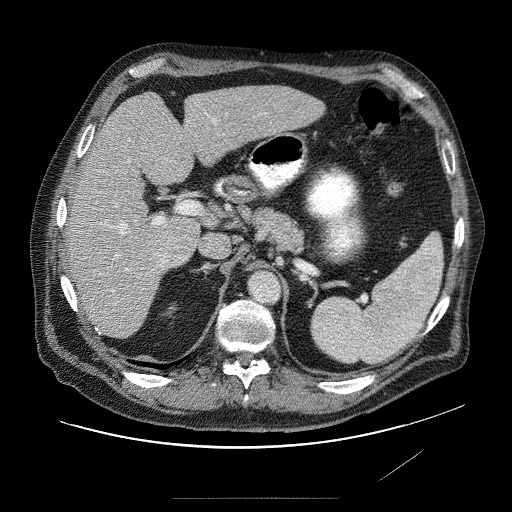
Contrast-enhanced abdominal CT (liver protocol), one axial slice. Slice 45 of 89 in the series (ordered by position). 120 kVp. Soft-tissue window (W 400 / L 40 HU). 2.5 mm slice thickness. 512 × 512 image matrix, field of view 420 × 420 mm. Case-level facts recorded for this patient, not image findings: diagnosis: hepatocellular carcinoma (patient treated with transarterial chemoembolisation; whether this scan precedes or follows treatment is not stated here); TNM stage (as recorded): Stage-IVA; Child-Pugh class: A; tumour differentiation: moderately differentiated.
Annotated regions visible in this slice (semi-automatically segmented with operator editing):
- liver parenchyma outside the tumour (the mass and vessels are separate outlines, so this box may not span the whole liver): bounding box [x1, y1, x2, y2] px = [62, 84, 326, 336]
- mass: [148, 142, 199, 266]
- liver vessels: [100, 115, 279, 302]